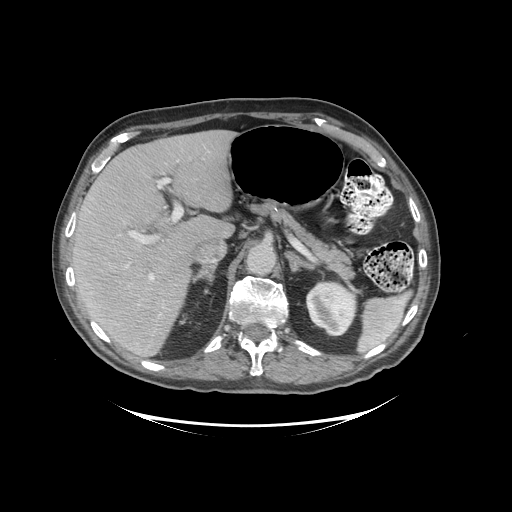
Contrast-enhanced abdominal CT (liver protocol), one axial slice. Slice 64 of 99 in the series (ordered by position). Reconstruction kernel STANDARD. 140 kVp. Soft-tissue window (W 400 / L 40 HU). 2.5 mm slice thickness. 512 × 512 image matrix, field of view 460 × 460 mm. From the clinical record (not read from this slice): diagnosis: hepatocellular carcinoma (patient treated with transarterial chemoembolisation; whether this scan precedes or follows treatment is not stated here); TNM stage (as recorded): Stage-I; Child-Pugh class: A.
Annotated regions visible in this slice (semi-automatic segmentation, software-assisted and operator-edited):
- liver parenchyma outside the tumour (the mass and vessels are separate outlines, so this box may not span the whole liver): bounding box (x1, y1, x2, y2) in pixels: (72, 130, 234, 356)
- mass: (90, 267, 149, 336)
- liver vessels: (89, 178, 178, 306)